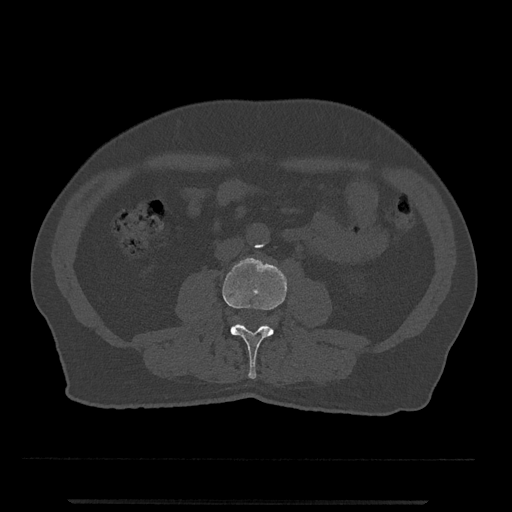
CT including the spine, one axial slice. Slice 189 of 797 in the series (ordered by position). Bone window (W 1800 / L 400 HU). 0.5 mm slice thickness. 512 × 512 image matrix, field of view 419 × 419 mm. Patient: male, 63 years. Case-level facts recorded for this patient, not image findings: primary cancer: prostate.
Annotated regions visible in this slice (semi-automatically segmented with operator editing):
- L3 vertebra: bounding box (x1, y1, x2, y2) in pixels: (222, 257, 287, 379)